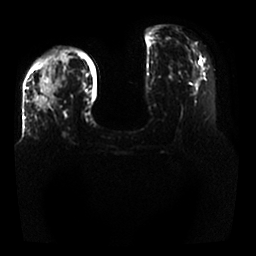
Breast MRI, one axial slice. Slice 10 of 25 in the series (ordered by position). Diffusion-weighted series; image 2 of 4 stored at this slice position (different b-values; order by instance number). 1.5 T. 4 mm slice thickness. 256 × 256 image matrix. Female patient.
Outlined on this slice (outlined manually by an expert reader):
- tumour on diffusion-weighted imaging: bounding box (x1, y1, x2, y2) in pixels: (35, 56, 69, 113)